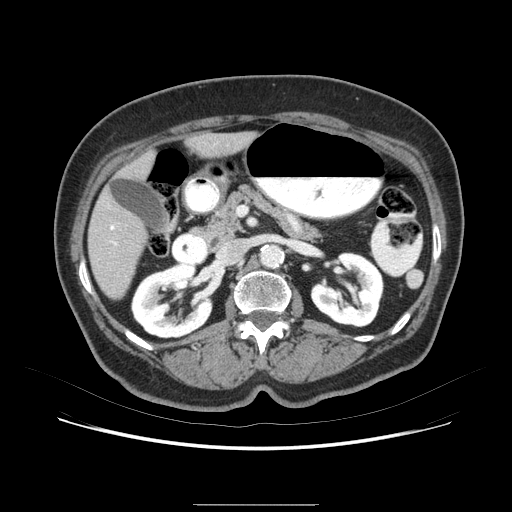
Contrast-enhanced abdominal CT (liver protocol), one axial slice; slice 30 of 79 in the series (ordered by position); soft-tissue window (W 400 / L 40 HU); 2.5 mm slice thickness; 512 × 512 image matrix, field of view 380 × 380 mm. From the clinical record (not read from this slice): diagnosis: hepatocellular carcinoma (patient treated with transarterial chemoembolisation; whether this scan precedes or follows treatment is not stated here); TNM stage (as recorded): Stage-I.
Outlined on this slice (semi-automatic segmentation, software-assisted and operator-edited):
- liver parenchyma outside the tumour (the mass and vessels are separate outlines, so this box may not span the whole liver): bounding box (x1, y1, x2, y2) in pixels: (86, 124, 268, 314)
- mass: (122, 206, 152, 231)
- liver vessels: (123, 147, 237, 273)